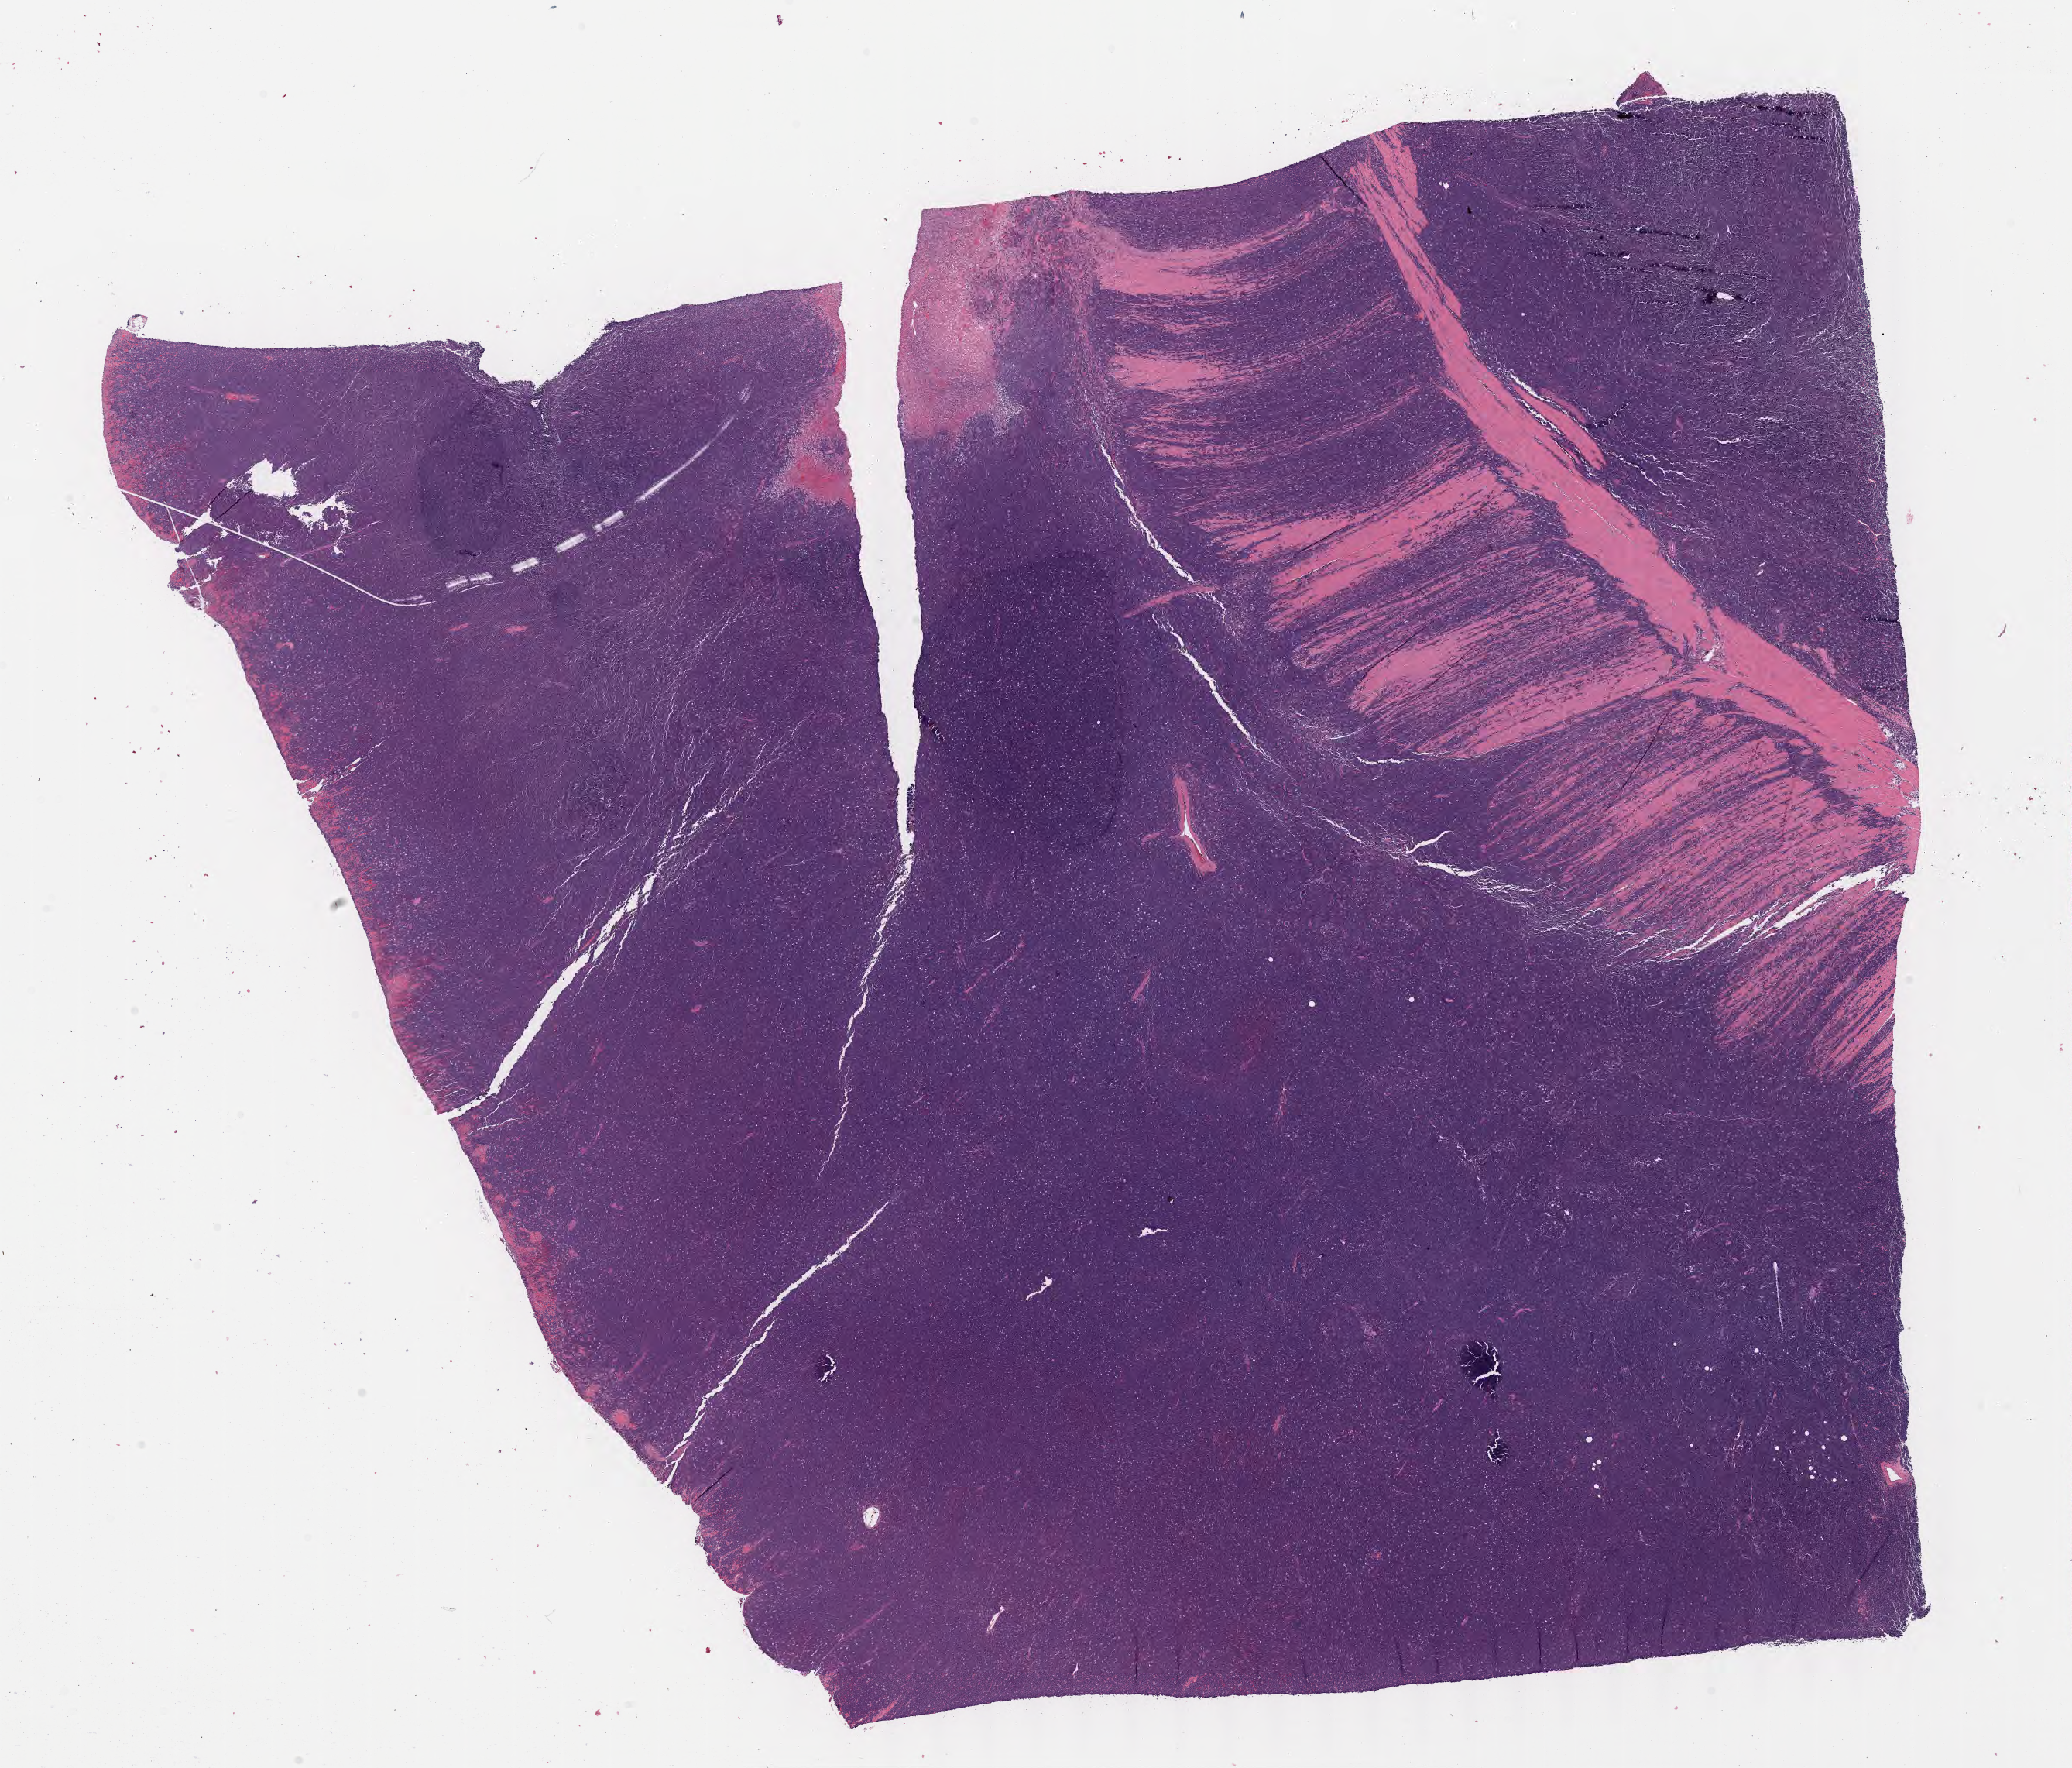
Whole-slide image, H&E stain, low-resolution overview of the scanned area, about 21.6 x 18.5 mm; tumor tissue; anatomic site: colon. Male patient, aged 14.
Histologic diagnosis: Burkitt lymphoma, NOS.